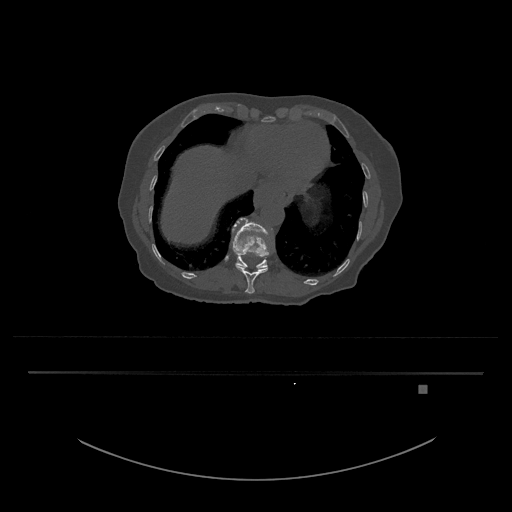
CT including the spine, one axial slice. Position 642 of 797 along the scan axis. 120 kVp. Bone window (W 1800 / L 400 HU). 512 × 512 image matrix, field of view 500 × 500 mm. Patient: female, 57 years. Case-level facts recorded for this patient, not image findings: primary cancer: cervical.
Structures marked on this image (semi-automatically segmented with operator editing):
- T11 vertebra: box from (x=236, y=264) to (x=268, y=294) px
- T12 vertebra: (x=232, y=217)–(x=270, y=269)